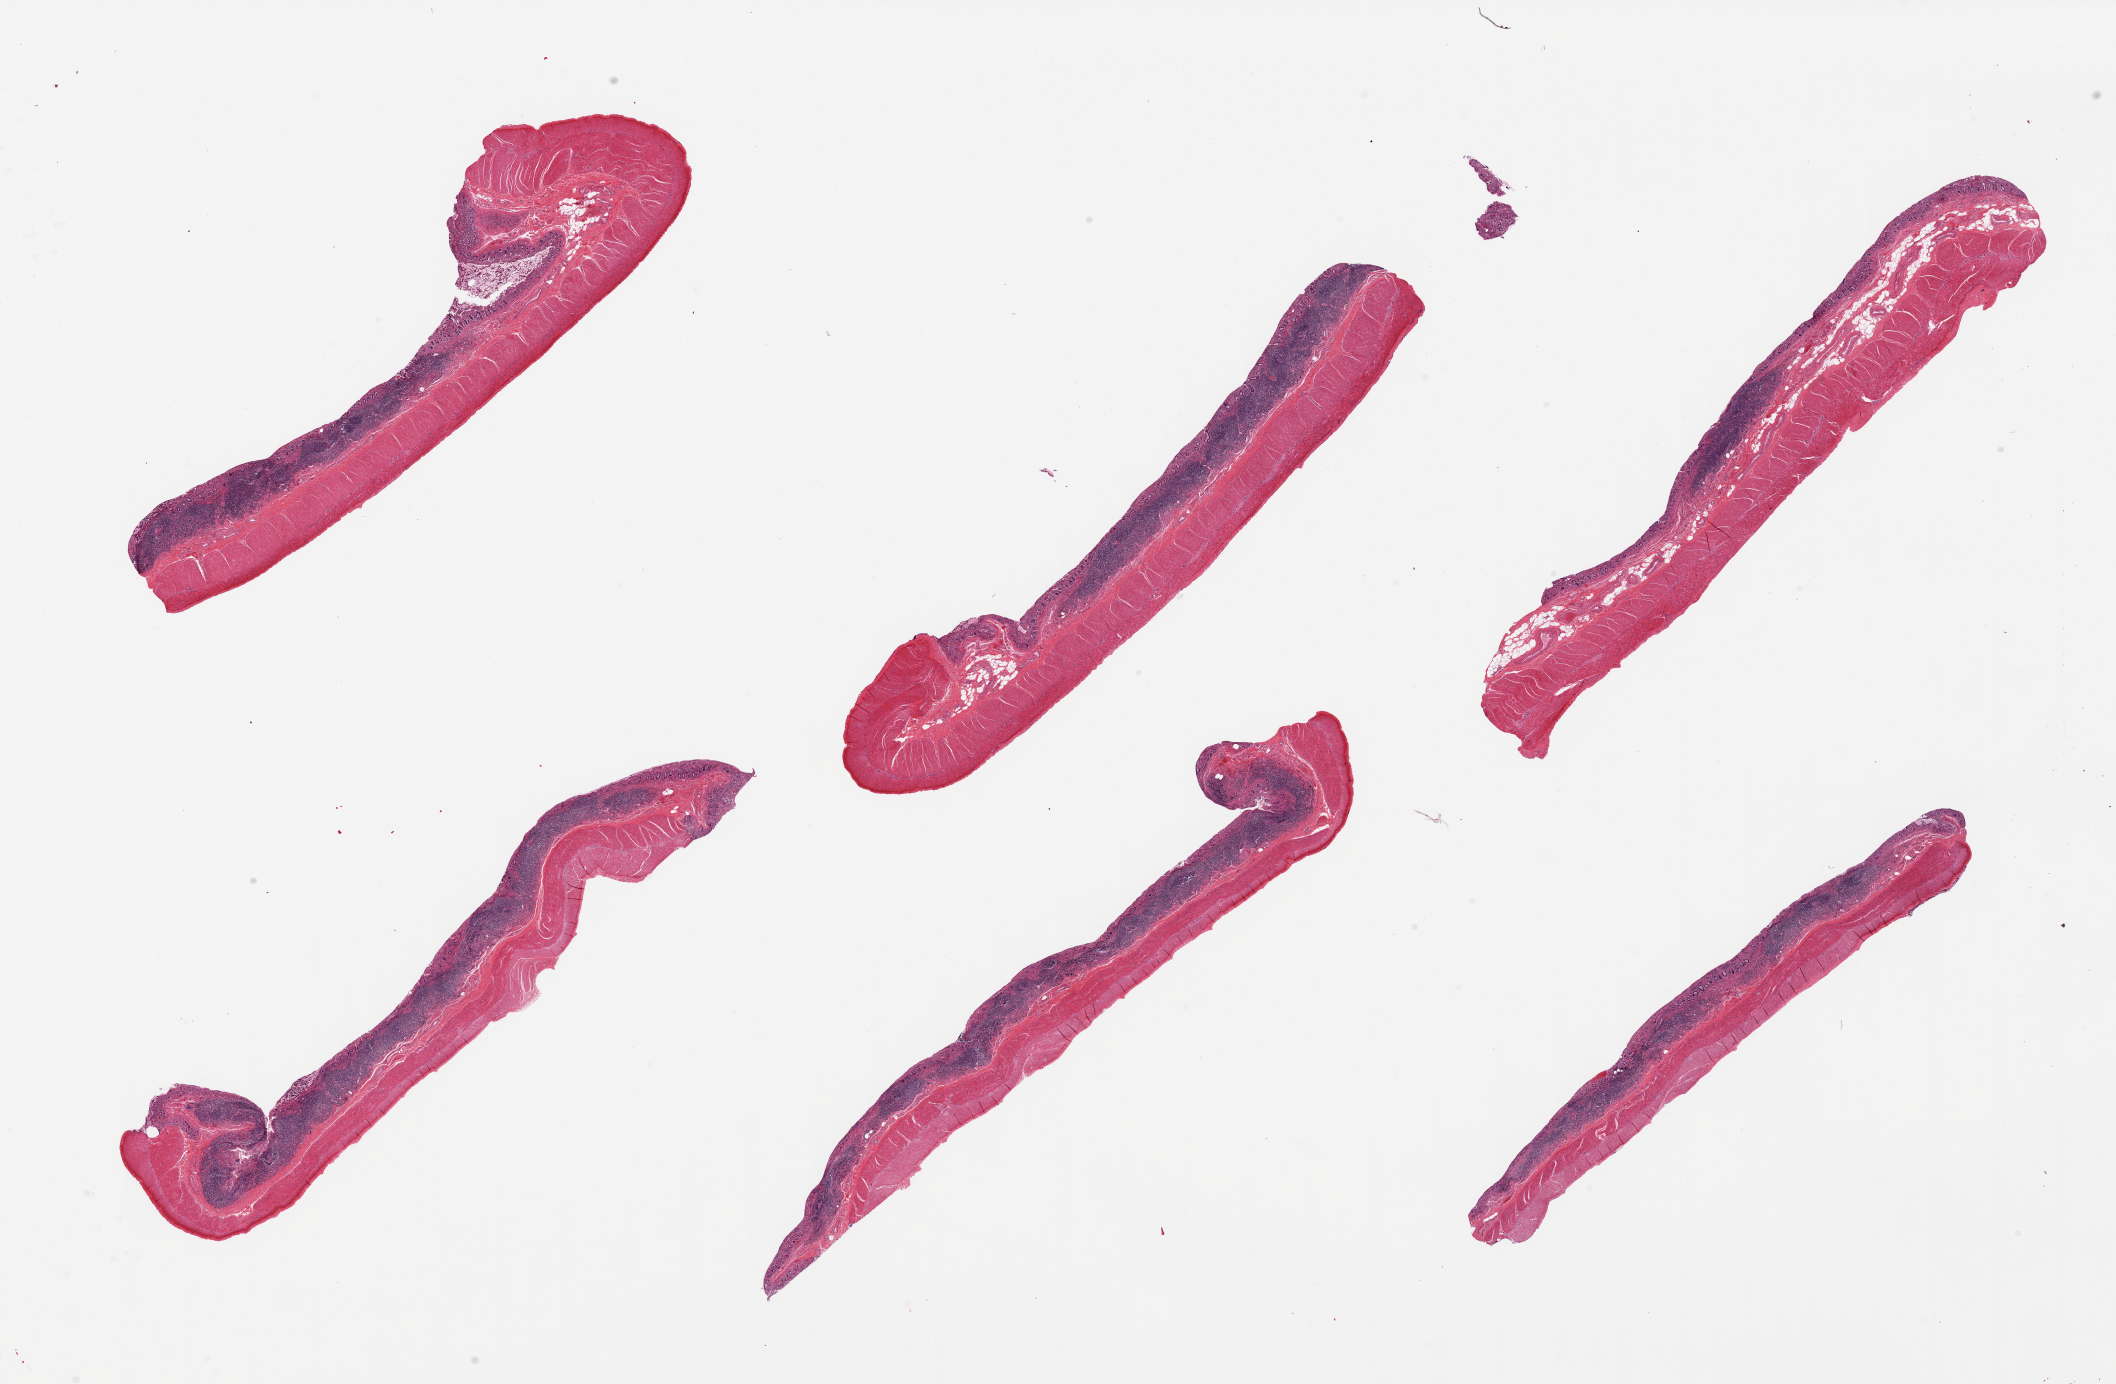
Whole-slide image, H&E stain — whole scanned area (about 33.5 x 21.9 mm, acquisition: 20x scan) shown as a low-resolution overview. PAXgene-fixed, paraffin-embedded tissue. Sampled site (target tissue): ileum. Donor tissue sample.
Reviewer comment on this tissue sample: 6 pieces, variably autolyzed and sloughed mucosa with prominent residual lymphoid tissue, muscularis (not target).